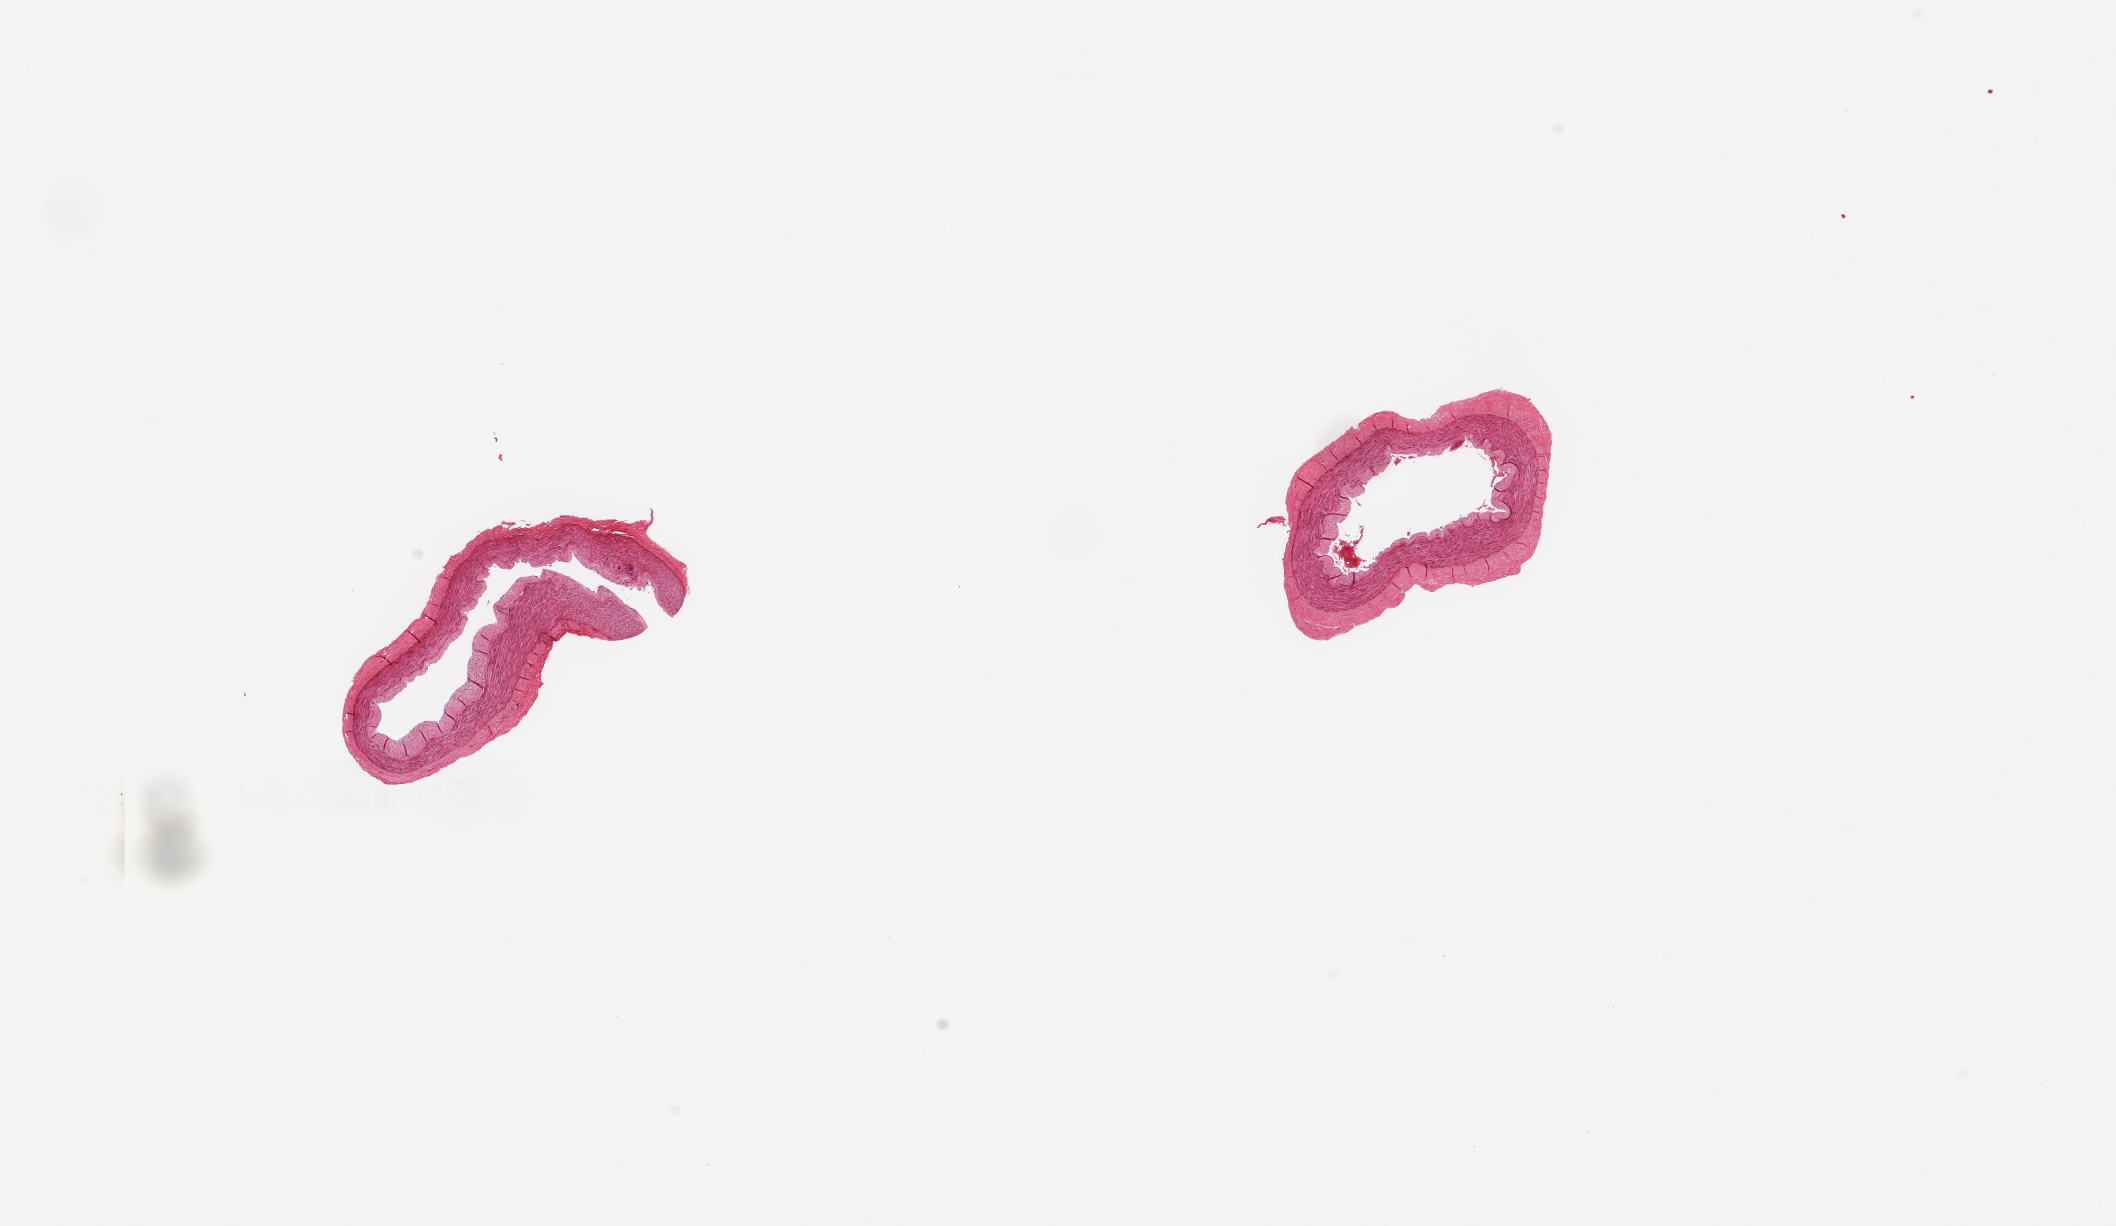
Hematoxylin and eosin (H&E) whole-slide image — whole scanned area (about 16.7 x 9.7 mm, acquisition: 20x scan) shown as a low-resolution overview. PAXgene-fixed paraffin-embedded (PFPE) section. Section of tibial artery (target tissue). Donor tissue sample. Male donor.
Review note (as recorded): 2 pieces, no adherent fat/atherosis.